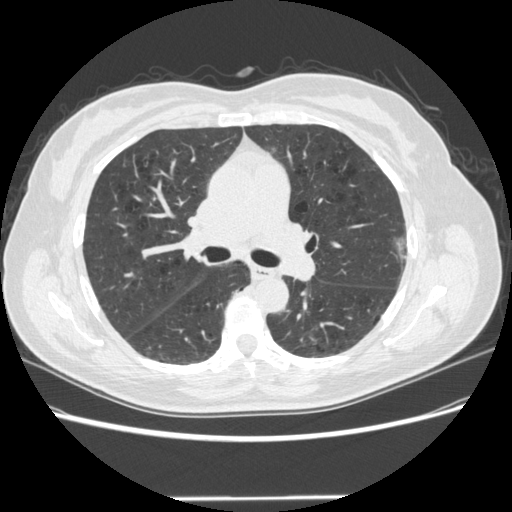
Chest CT (low-dose screening protocol), one axial image. Baseline screening round. Lung window (W 1500 / L -600 HU). Standard (soft-tissue) reconstruction kernel (STANDARD). 120 kVp. Slice 191 of 301 in the series. 512 × 512 image matrix, field of view 360 × 360 mm. Female, age 61 years at enrolment. Current smoker at enrolment.
- Expert-annotated lung lesion, box from (x=382, y=227) to (x=425, y=278) px.
- No non-calcified nodule or mass ≥4 mm was recorded by the screening reader at this exam.
- Official screen result: negative screen, minor abnormalities not suspicious for lung cancer.
- Lung cancer was diagnosed 791 days after this screen: bronchiolo-alveolar adenocarcinoma, NOS, left upper lobe, well differentiated (G1), stage IA (AJCC 6th edition), 11 mm at pathology.